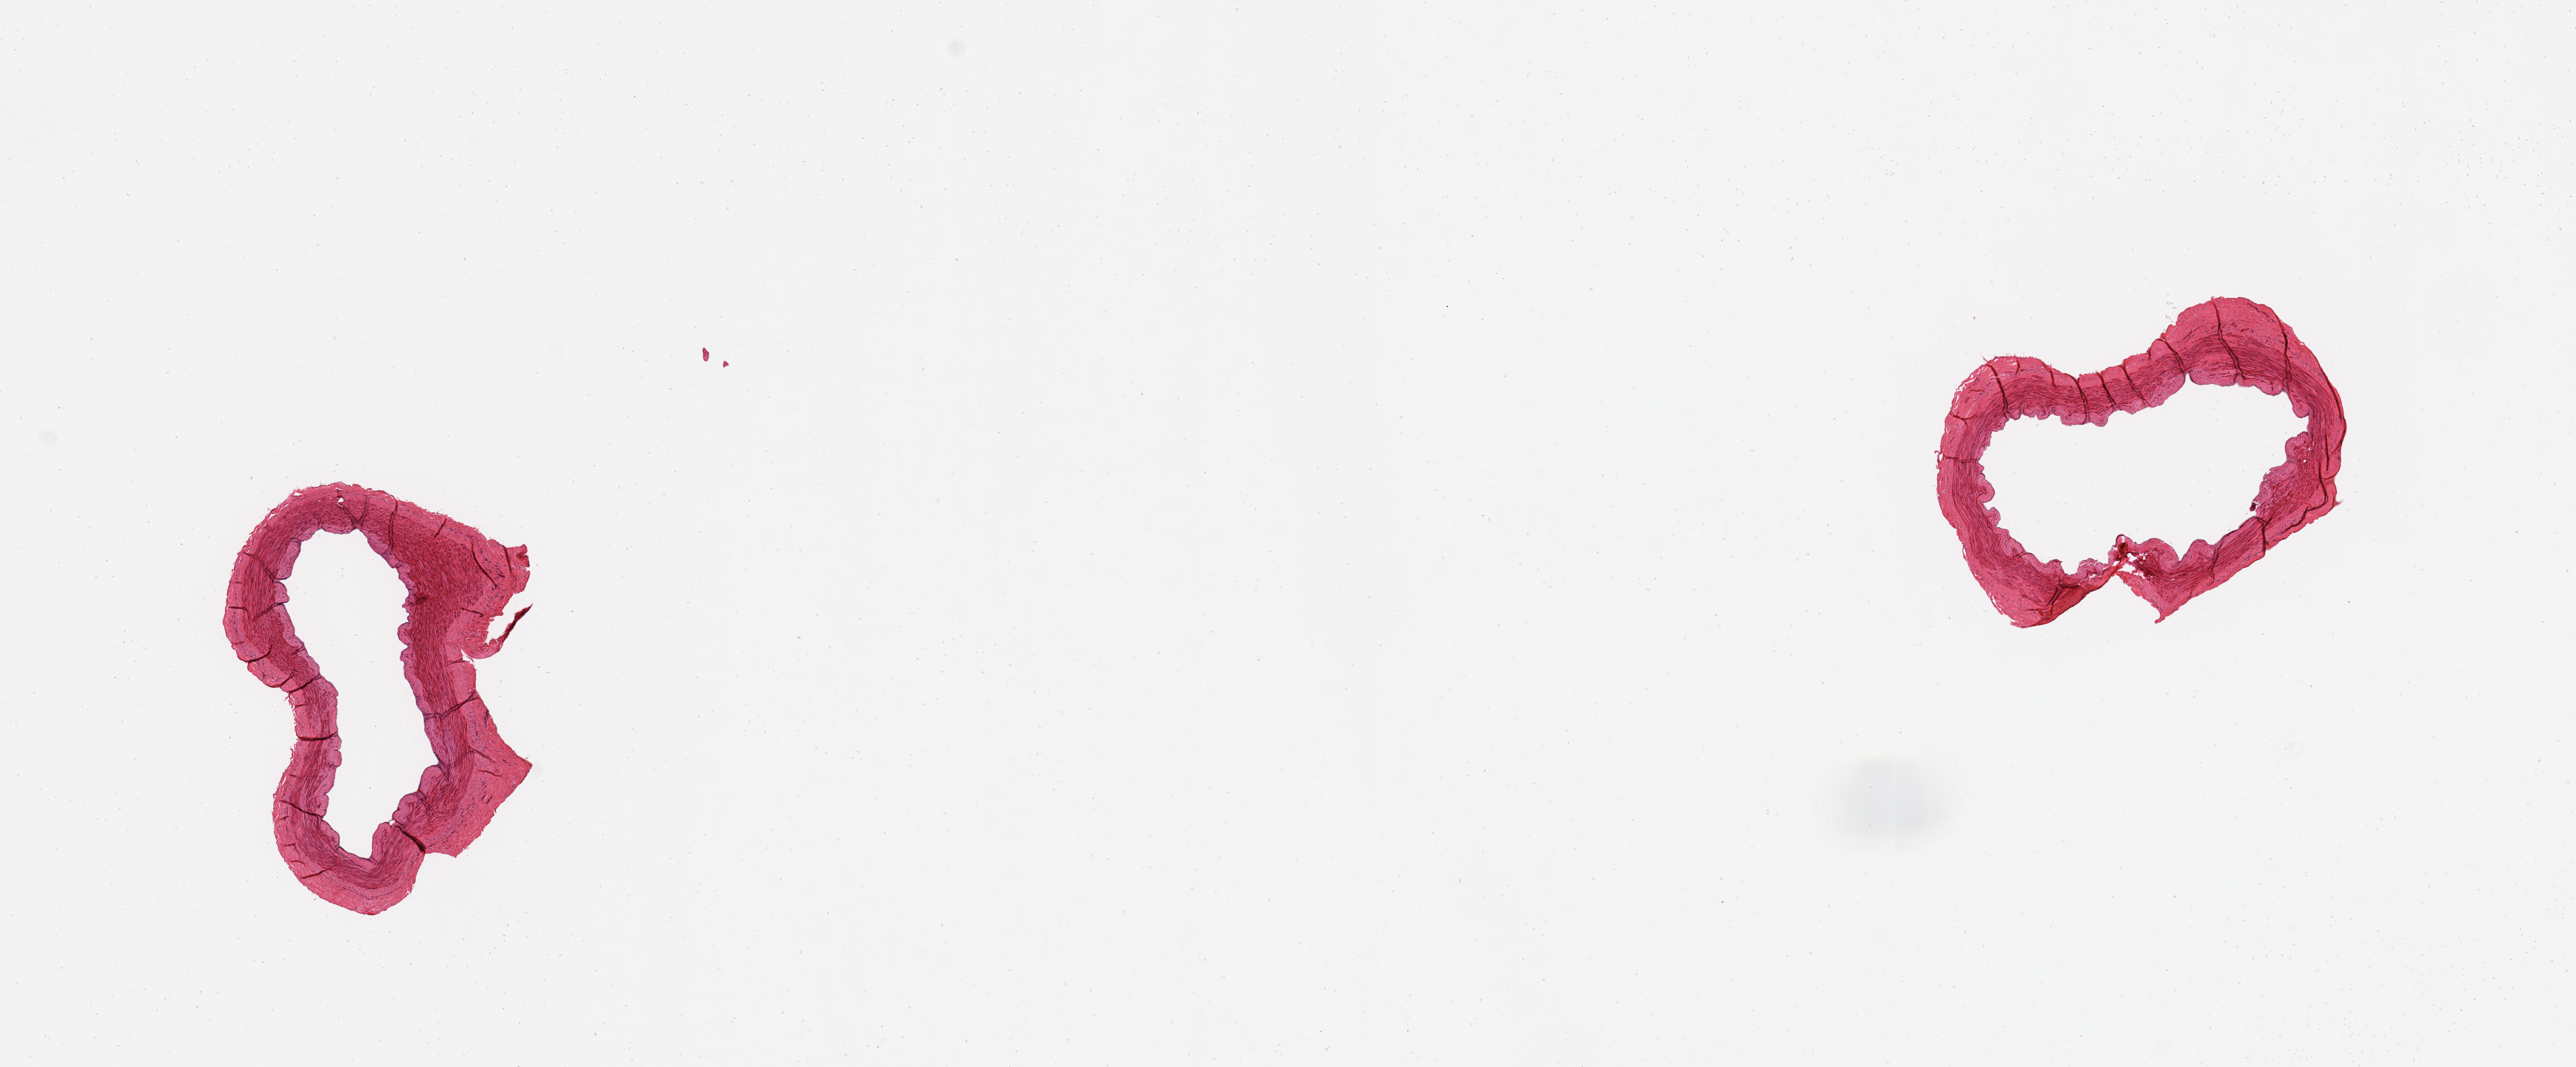
Digitized hematoxylin and eosin (H&E)-stained section — whole scanned area (about 14.8 x 6.1 mm) shown as a low-resolution overview, PAXgene-fixed paraffin-embedded (PFPE) section, target tissue: tibial artery, tissue donor sample. Donor: male.
Reviewer comment on this tissue sample: 2 pieces; well trimmed.